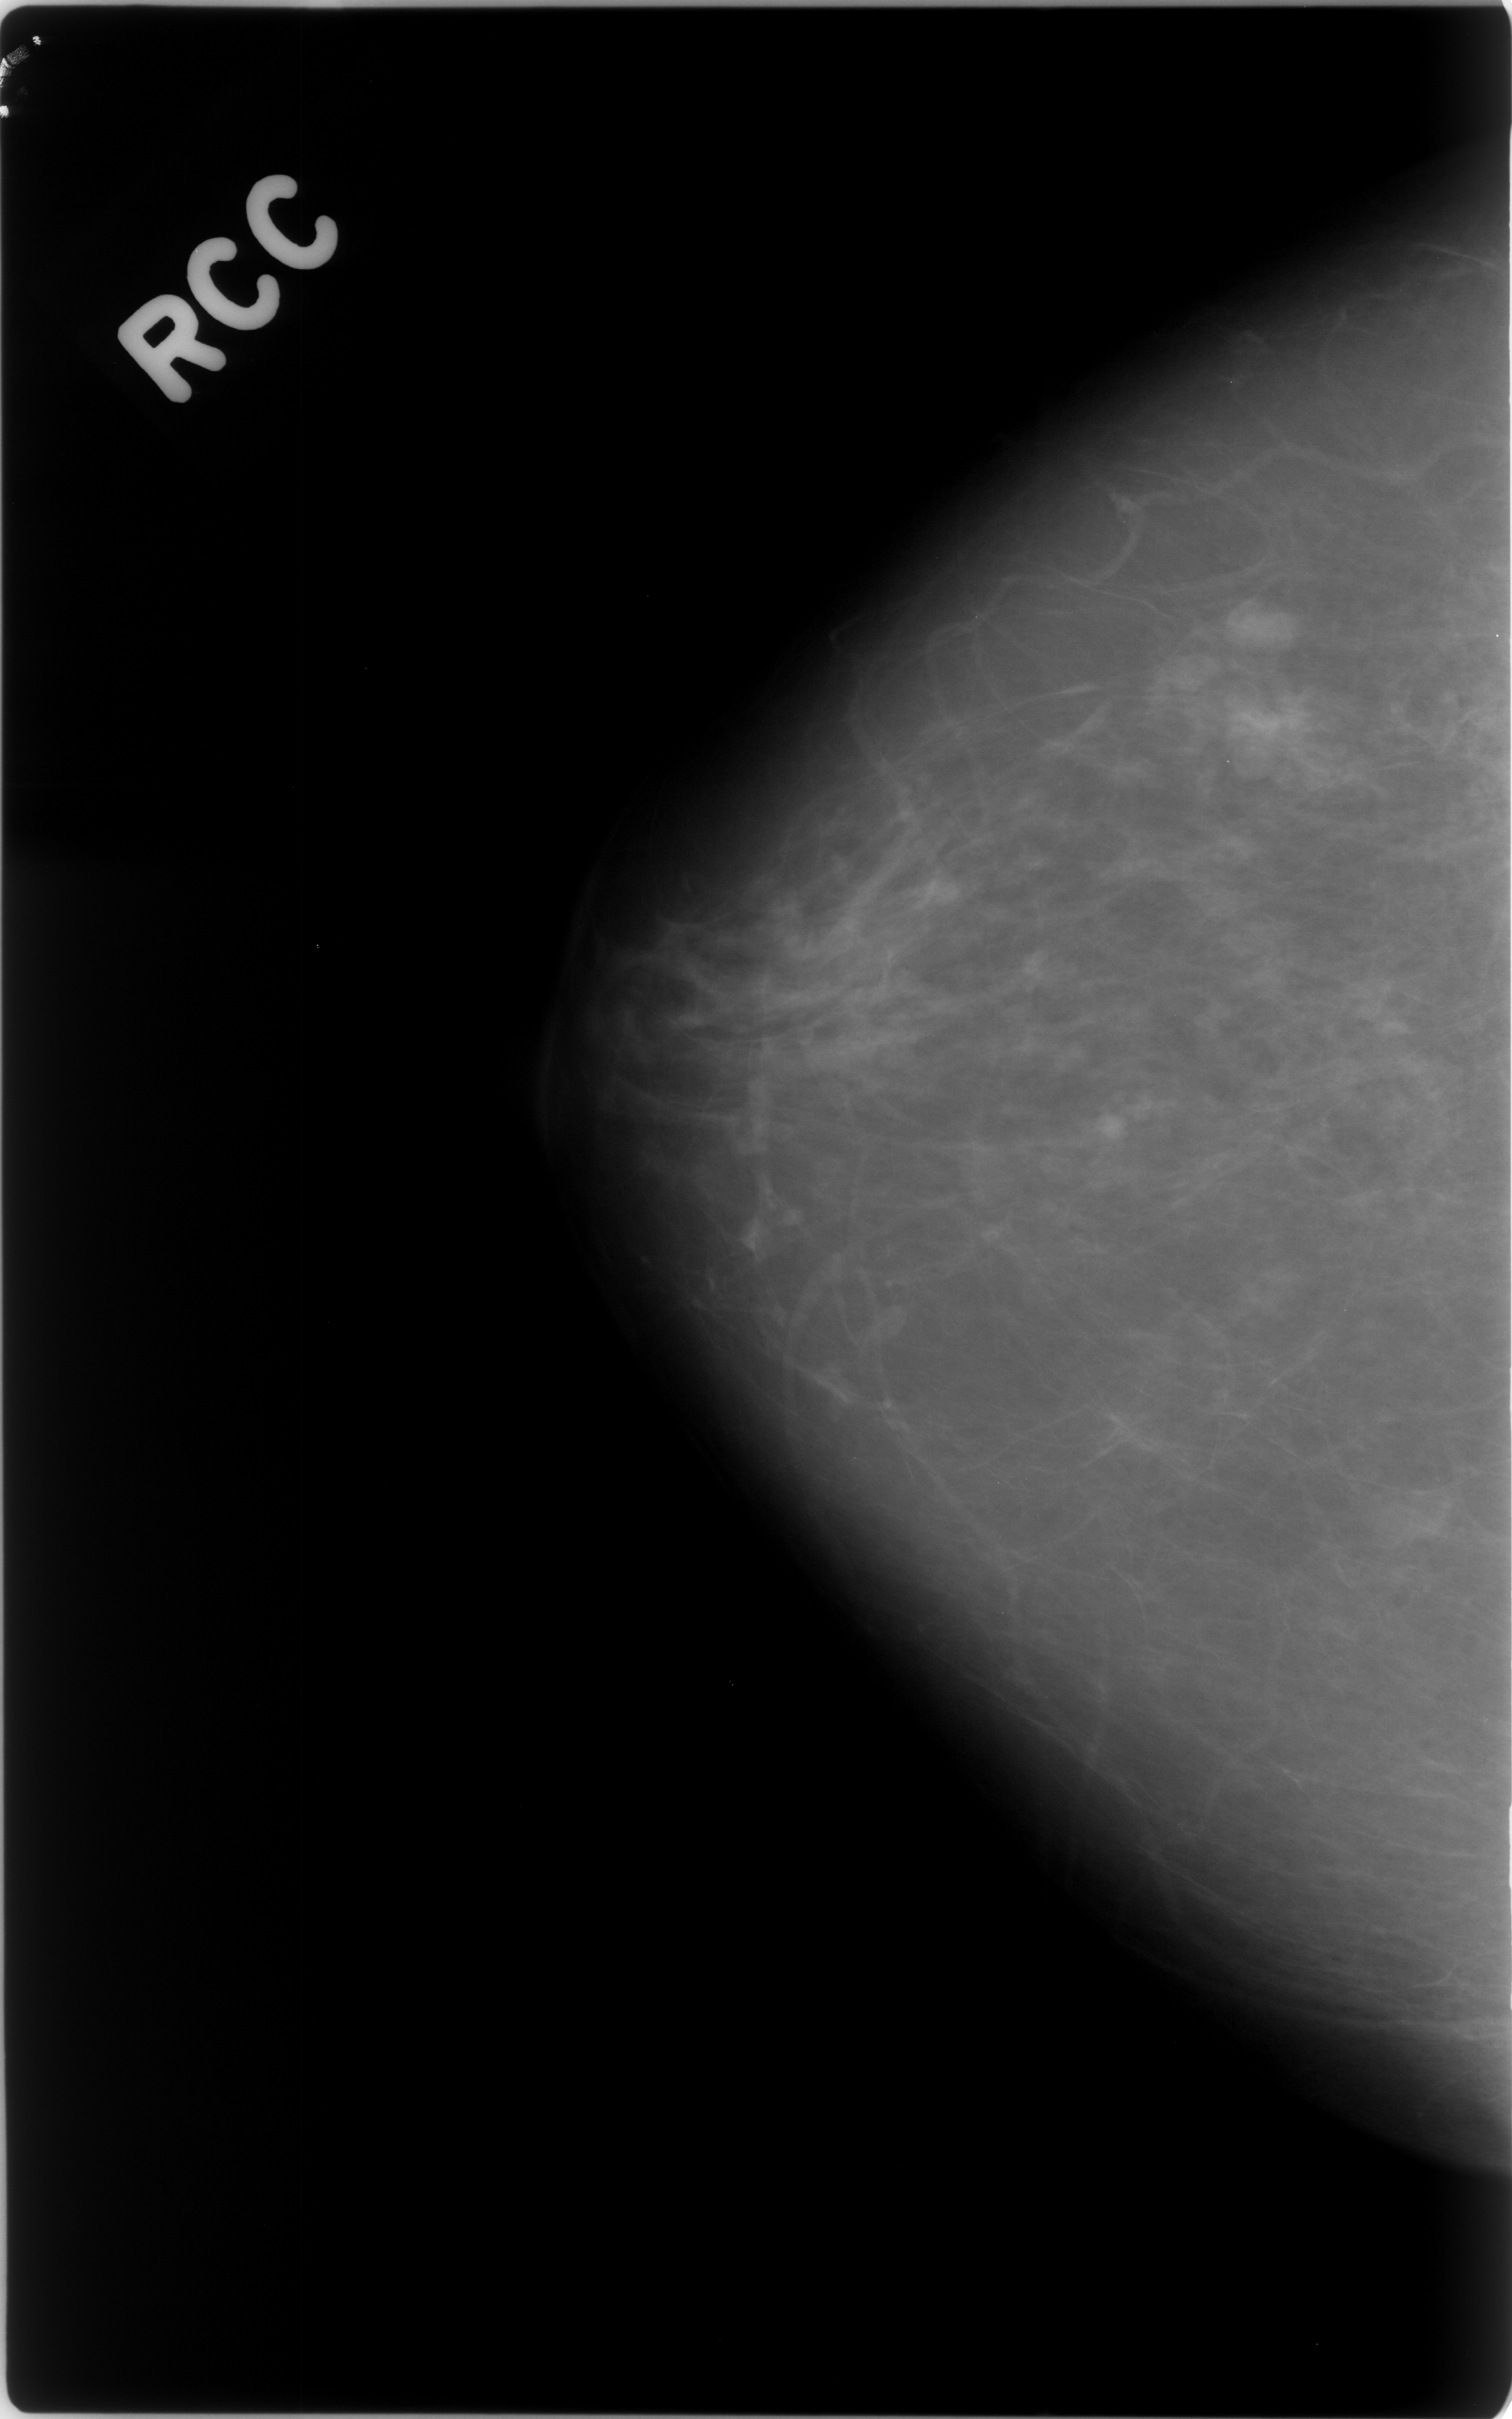
Mammogram (digitized film), right breast, craniocaudal (CC) view, BI-RADS breast density category 1 (scale 1–4).
- Abnormality record for this image: mass, shape lobulated, margins circumscribed; BI-RADS assessment category 3; benign without callback (not worked up further).